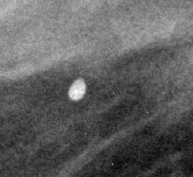
Region of interest cut from a scanned film mammogram (one marked finding), right breast, MLO view.
Finding: calcifications, morphology round and regular / lucent center; BI-RADS assessment category 2; benign; no additional work-up was recommended (benign without callback).